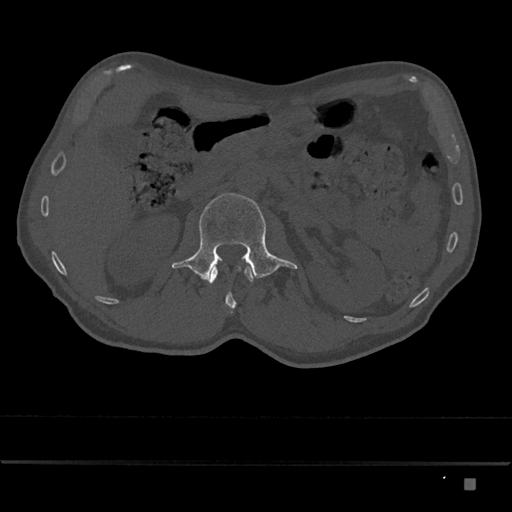
CT including the spine, one axial slice; 120 kVp; bone window (W 1800 / L 400 HU); 0.5 mm slice thickness; 512 × 512 image matrix, field of view 390 × 390 mm. Patient: male, 72 years. From the clinical record (not read from this slice): primary cancer: prostate.
Outlined on this slice (semi-automatically segmented with operator editing):
- L1 vertebra: bounding box <209,265,254,313> (left, top, right, bottom; pixels)
- L2 vertebra: <172,193,297,282>